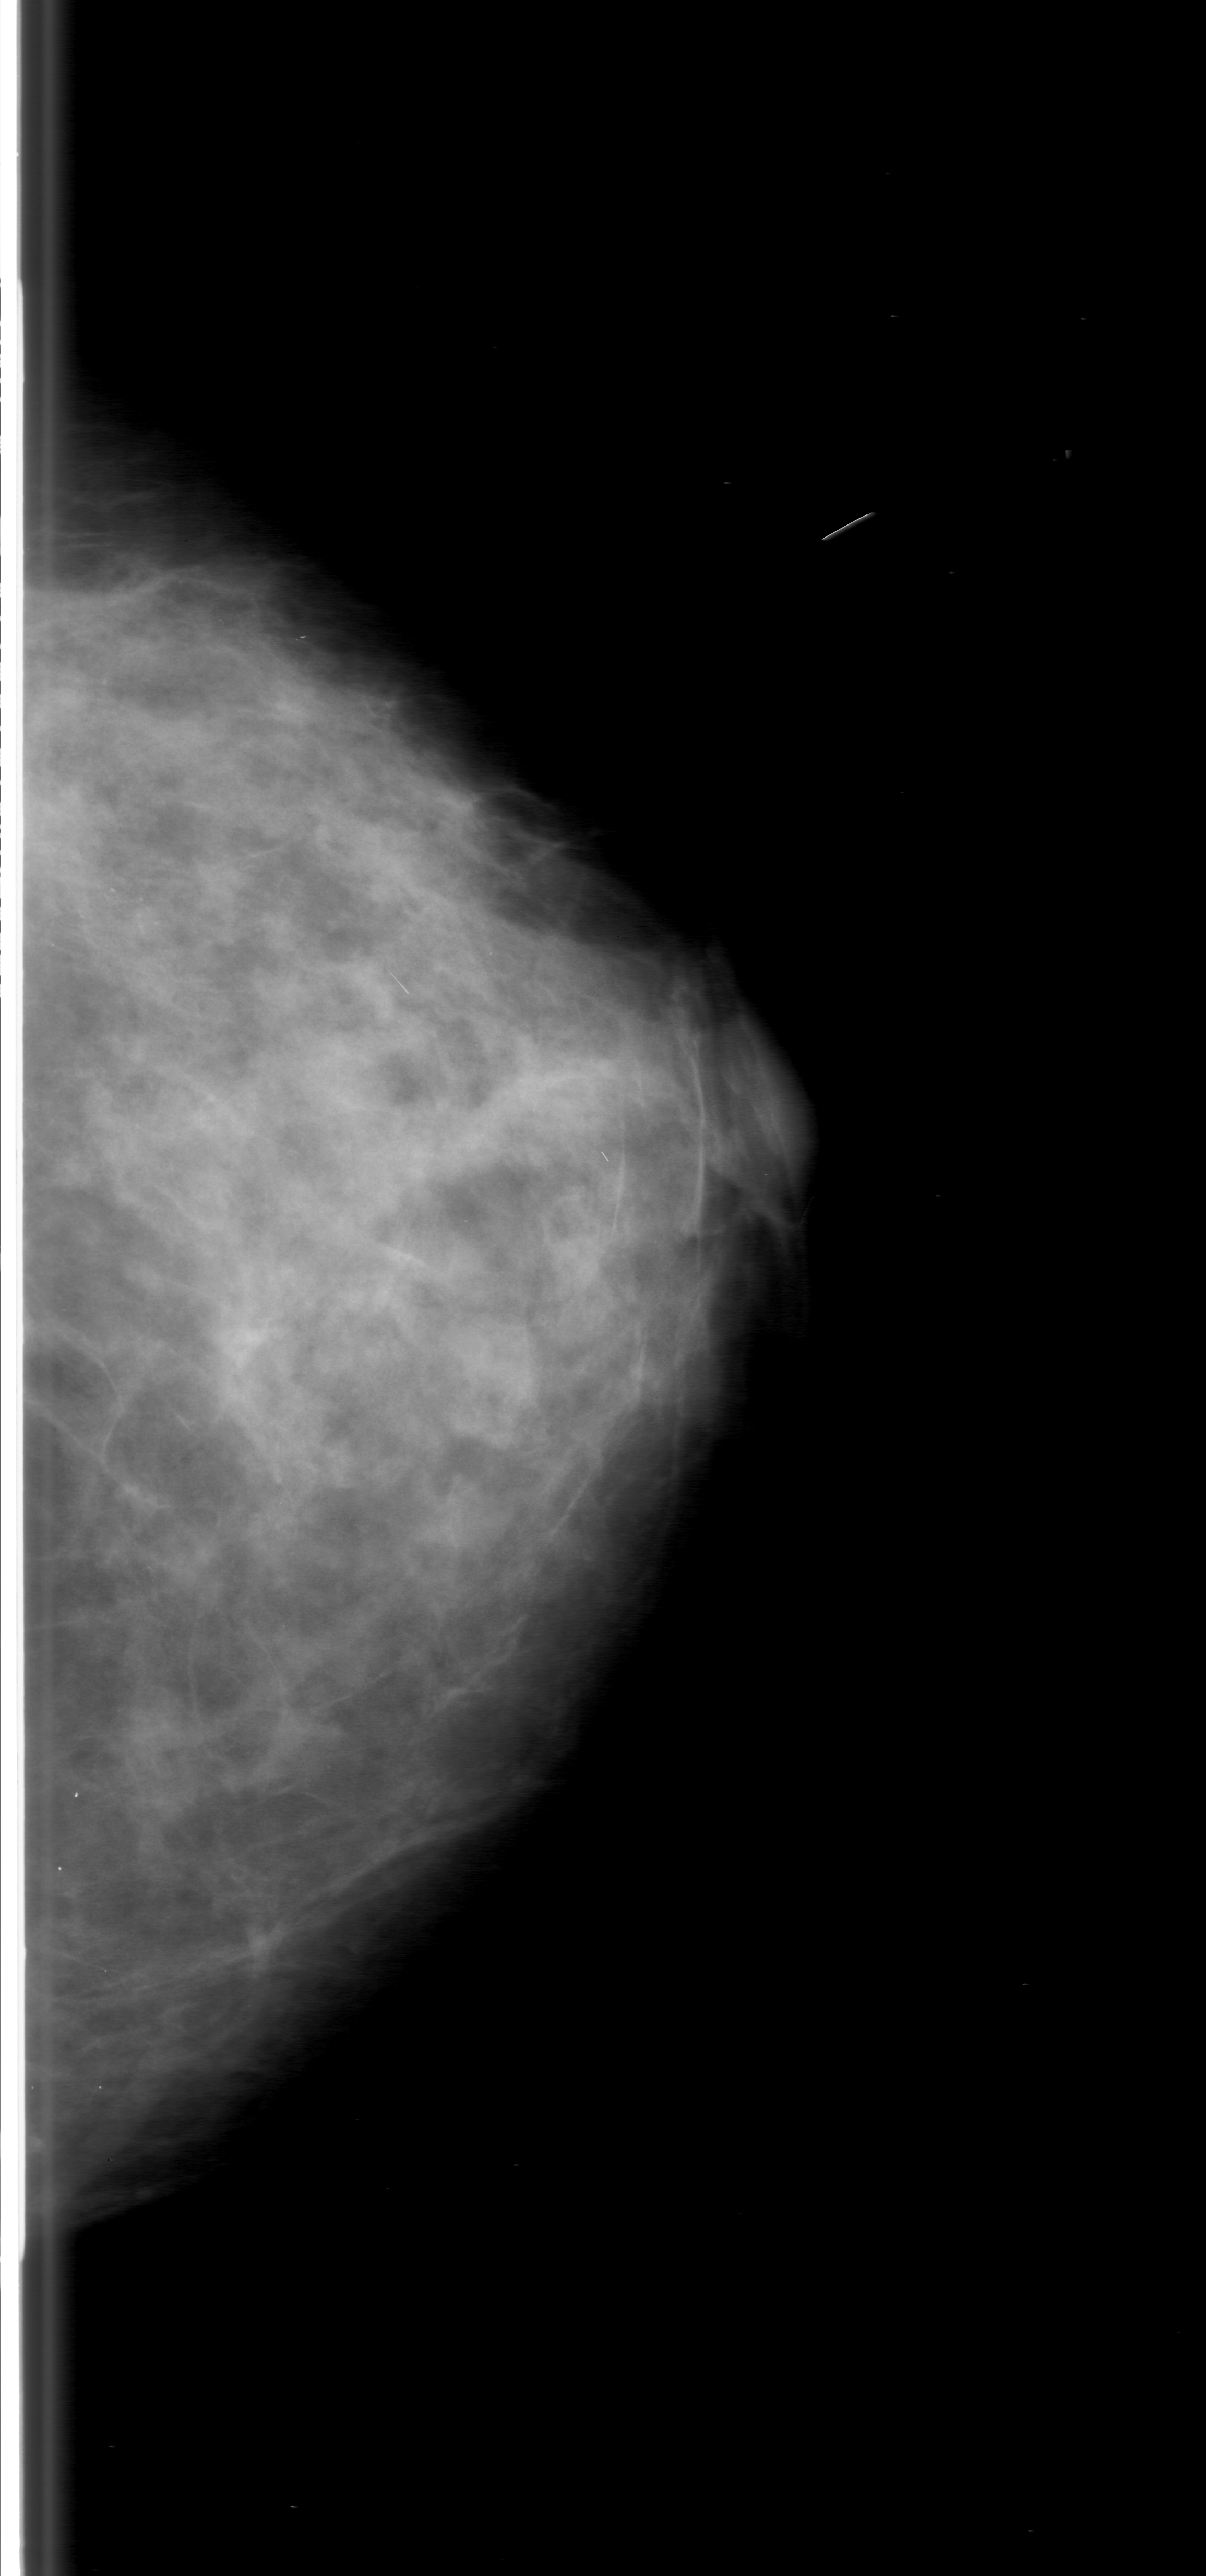
Mammogram (digitized film), left breast, craniocaudal (CC) view, breast composition: heterogeneously dense (BI-RADS density category 3 of 4).
Radiologist-marked abnormalities on this image: calcifications, morphology amorphous, distribution clustered; BI-RADS assessment category 3; subtlety rating 2 on a 1 (subtle) to 5 (obvious) scale; pathology result (as recorded, not read from the image): malignant.